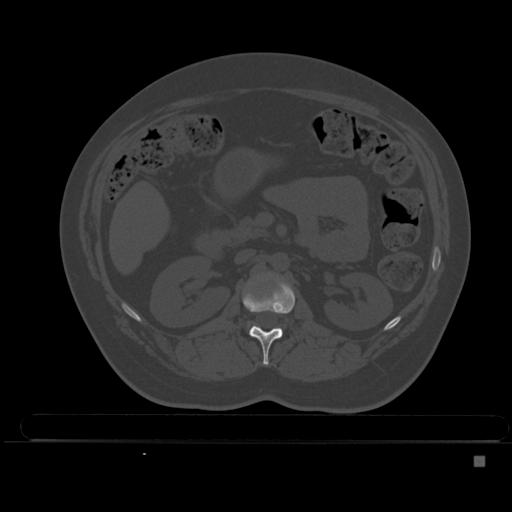
CT including the spine, one axial slice. Bone window (W 1800 / L 400 HU). 1.5 mm slice thickness. 512 × 512 image matrix. Patient: female, 33 years. Case-level facts recorded for this patient, not image findings: primary cancer: breast; vertebrae with lytic lesions (as recorded): T1.
Annotated regions visible in this slice (semi-automatically segmented with operator editing):
- L1 vertebra: box from (x=242, y=276) to (x=295, y=366) px